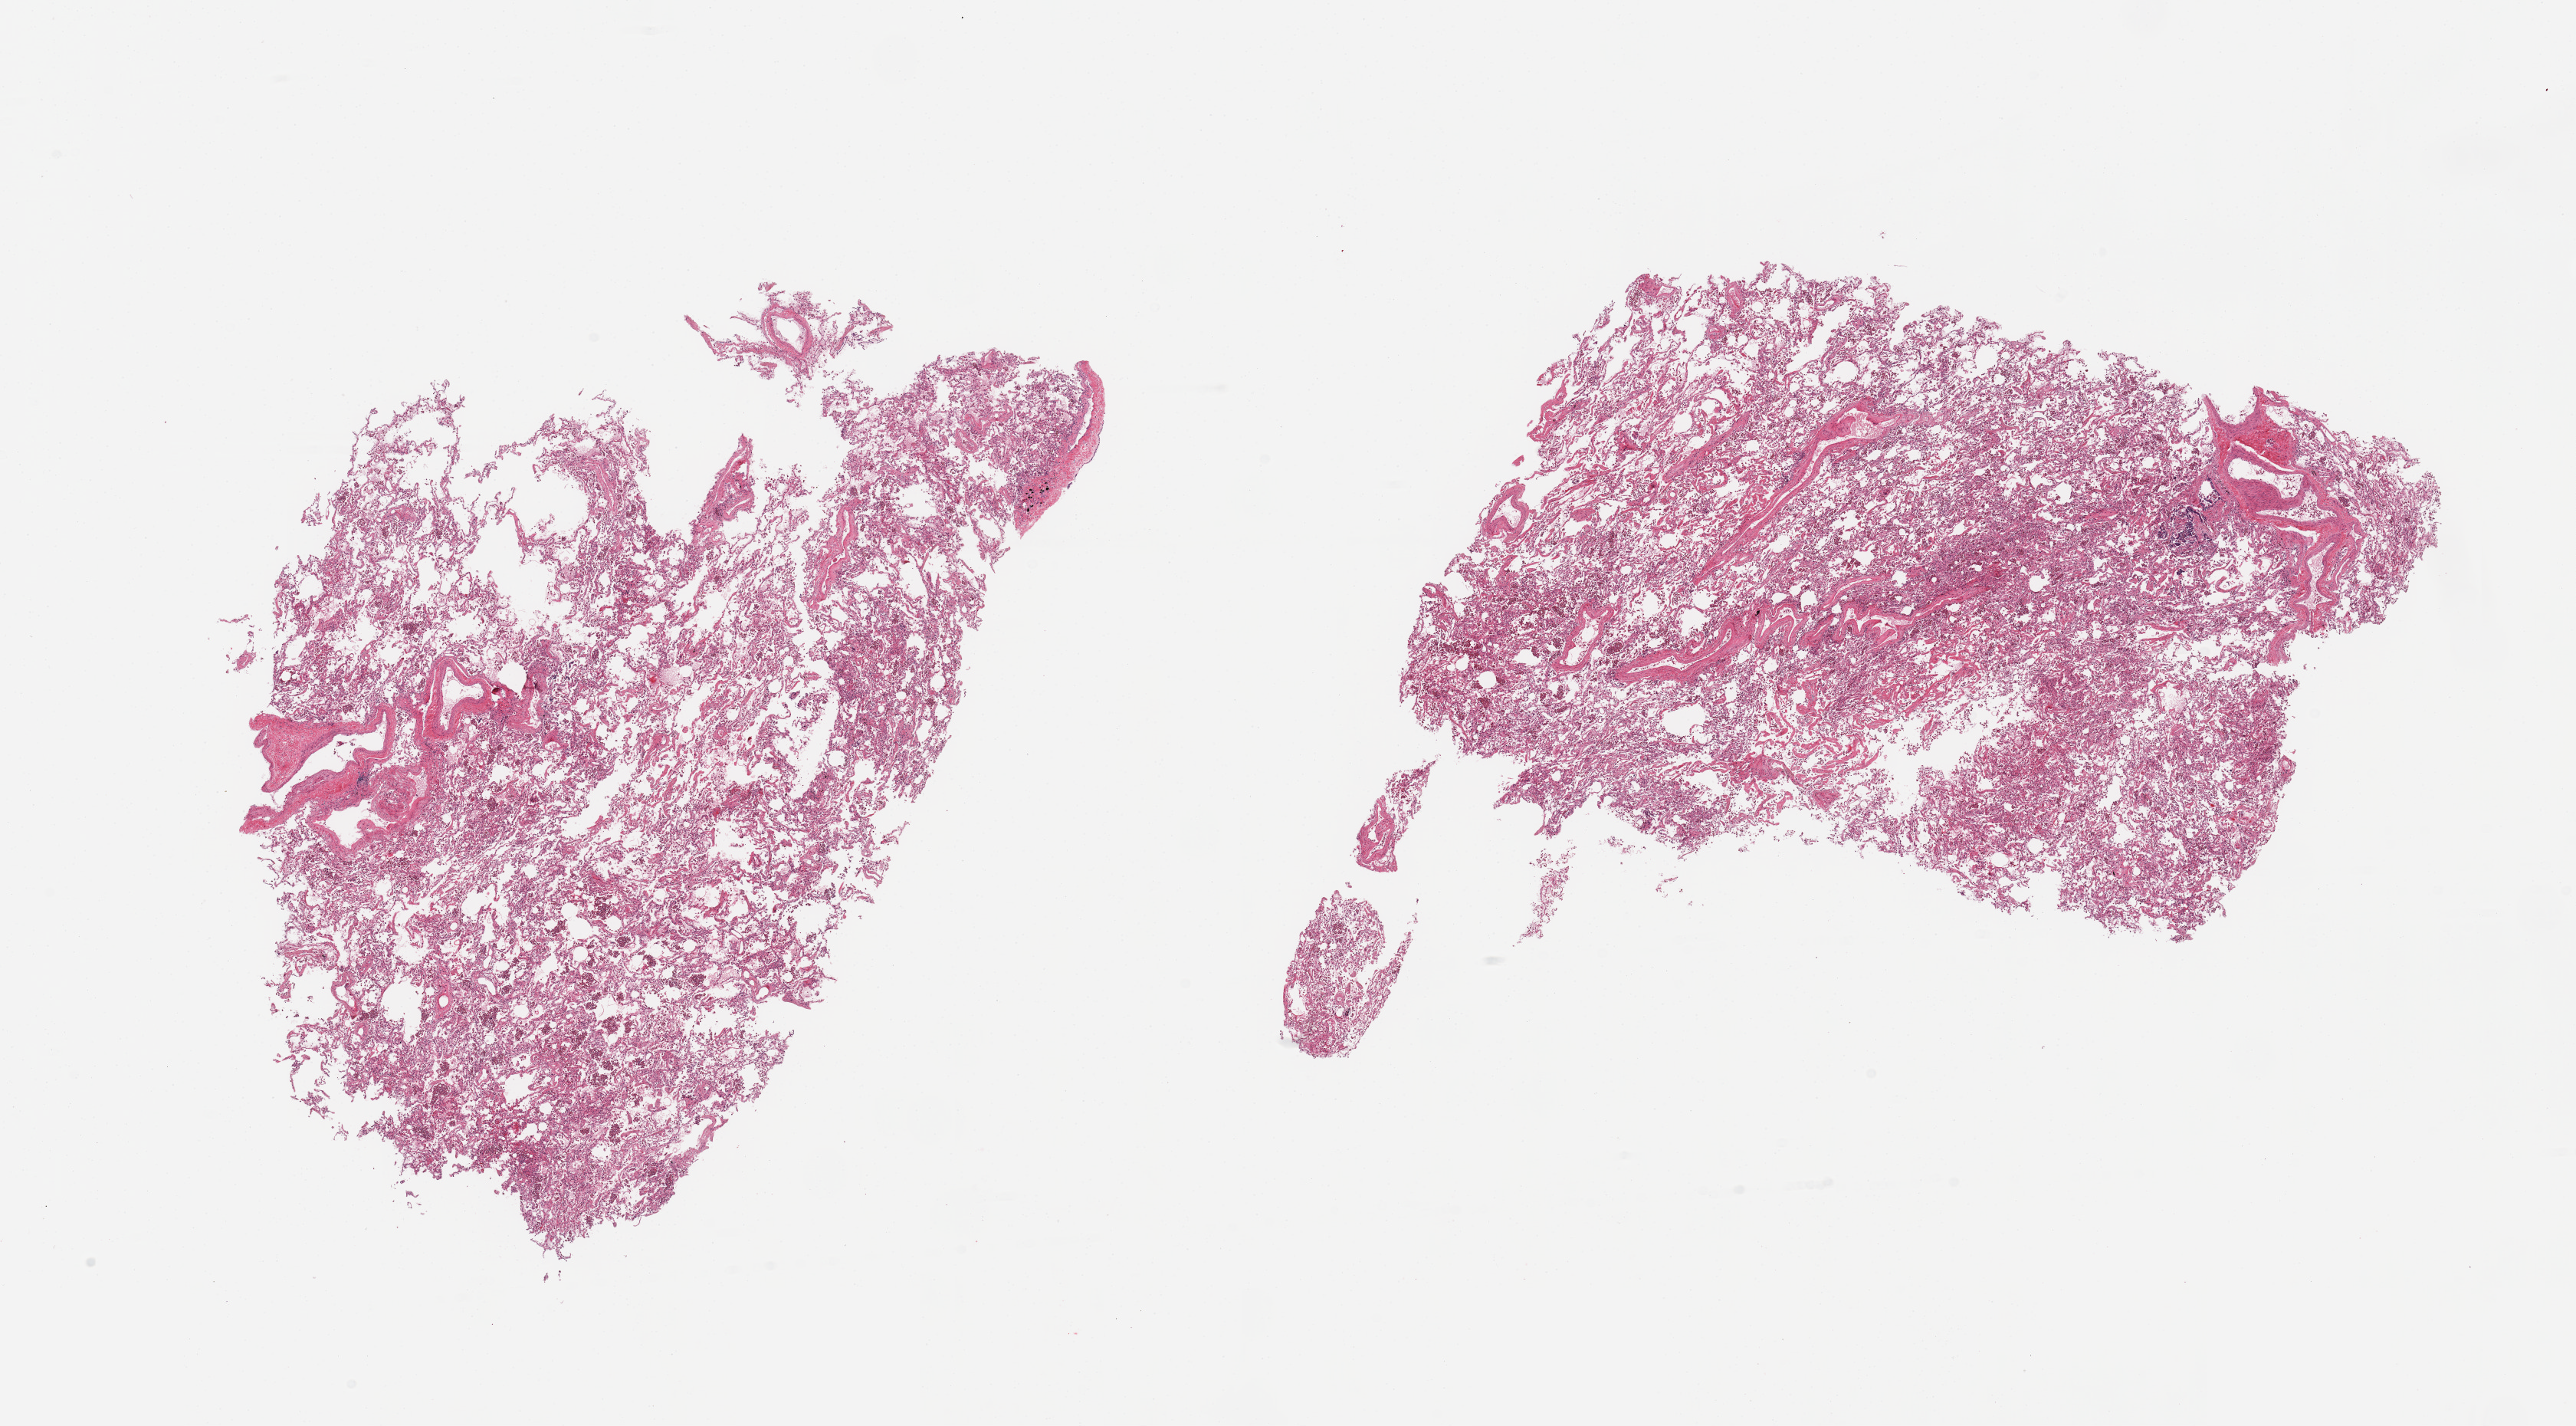
Digitized hematoxylin and eosin (H&E)-stained section — a low-resolution overview of the entire scanned area, about 26.6 x 14.7 mm. PAXgene-fixed, paraffin-embedded tissue. Sampled site (target tissue): lung. Tissue donor sample. Donor: male.
Pathologist's review note for this sample: 2 pieces; includes few larger vessels, many pigmented macrophages.